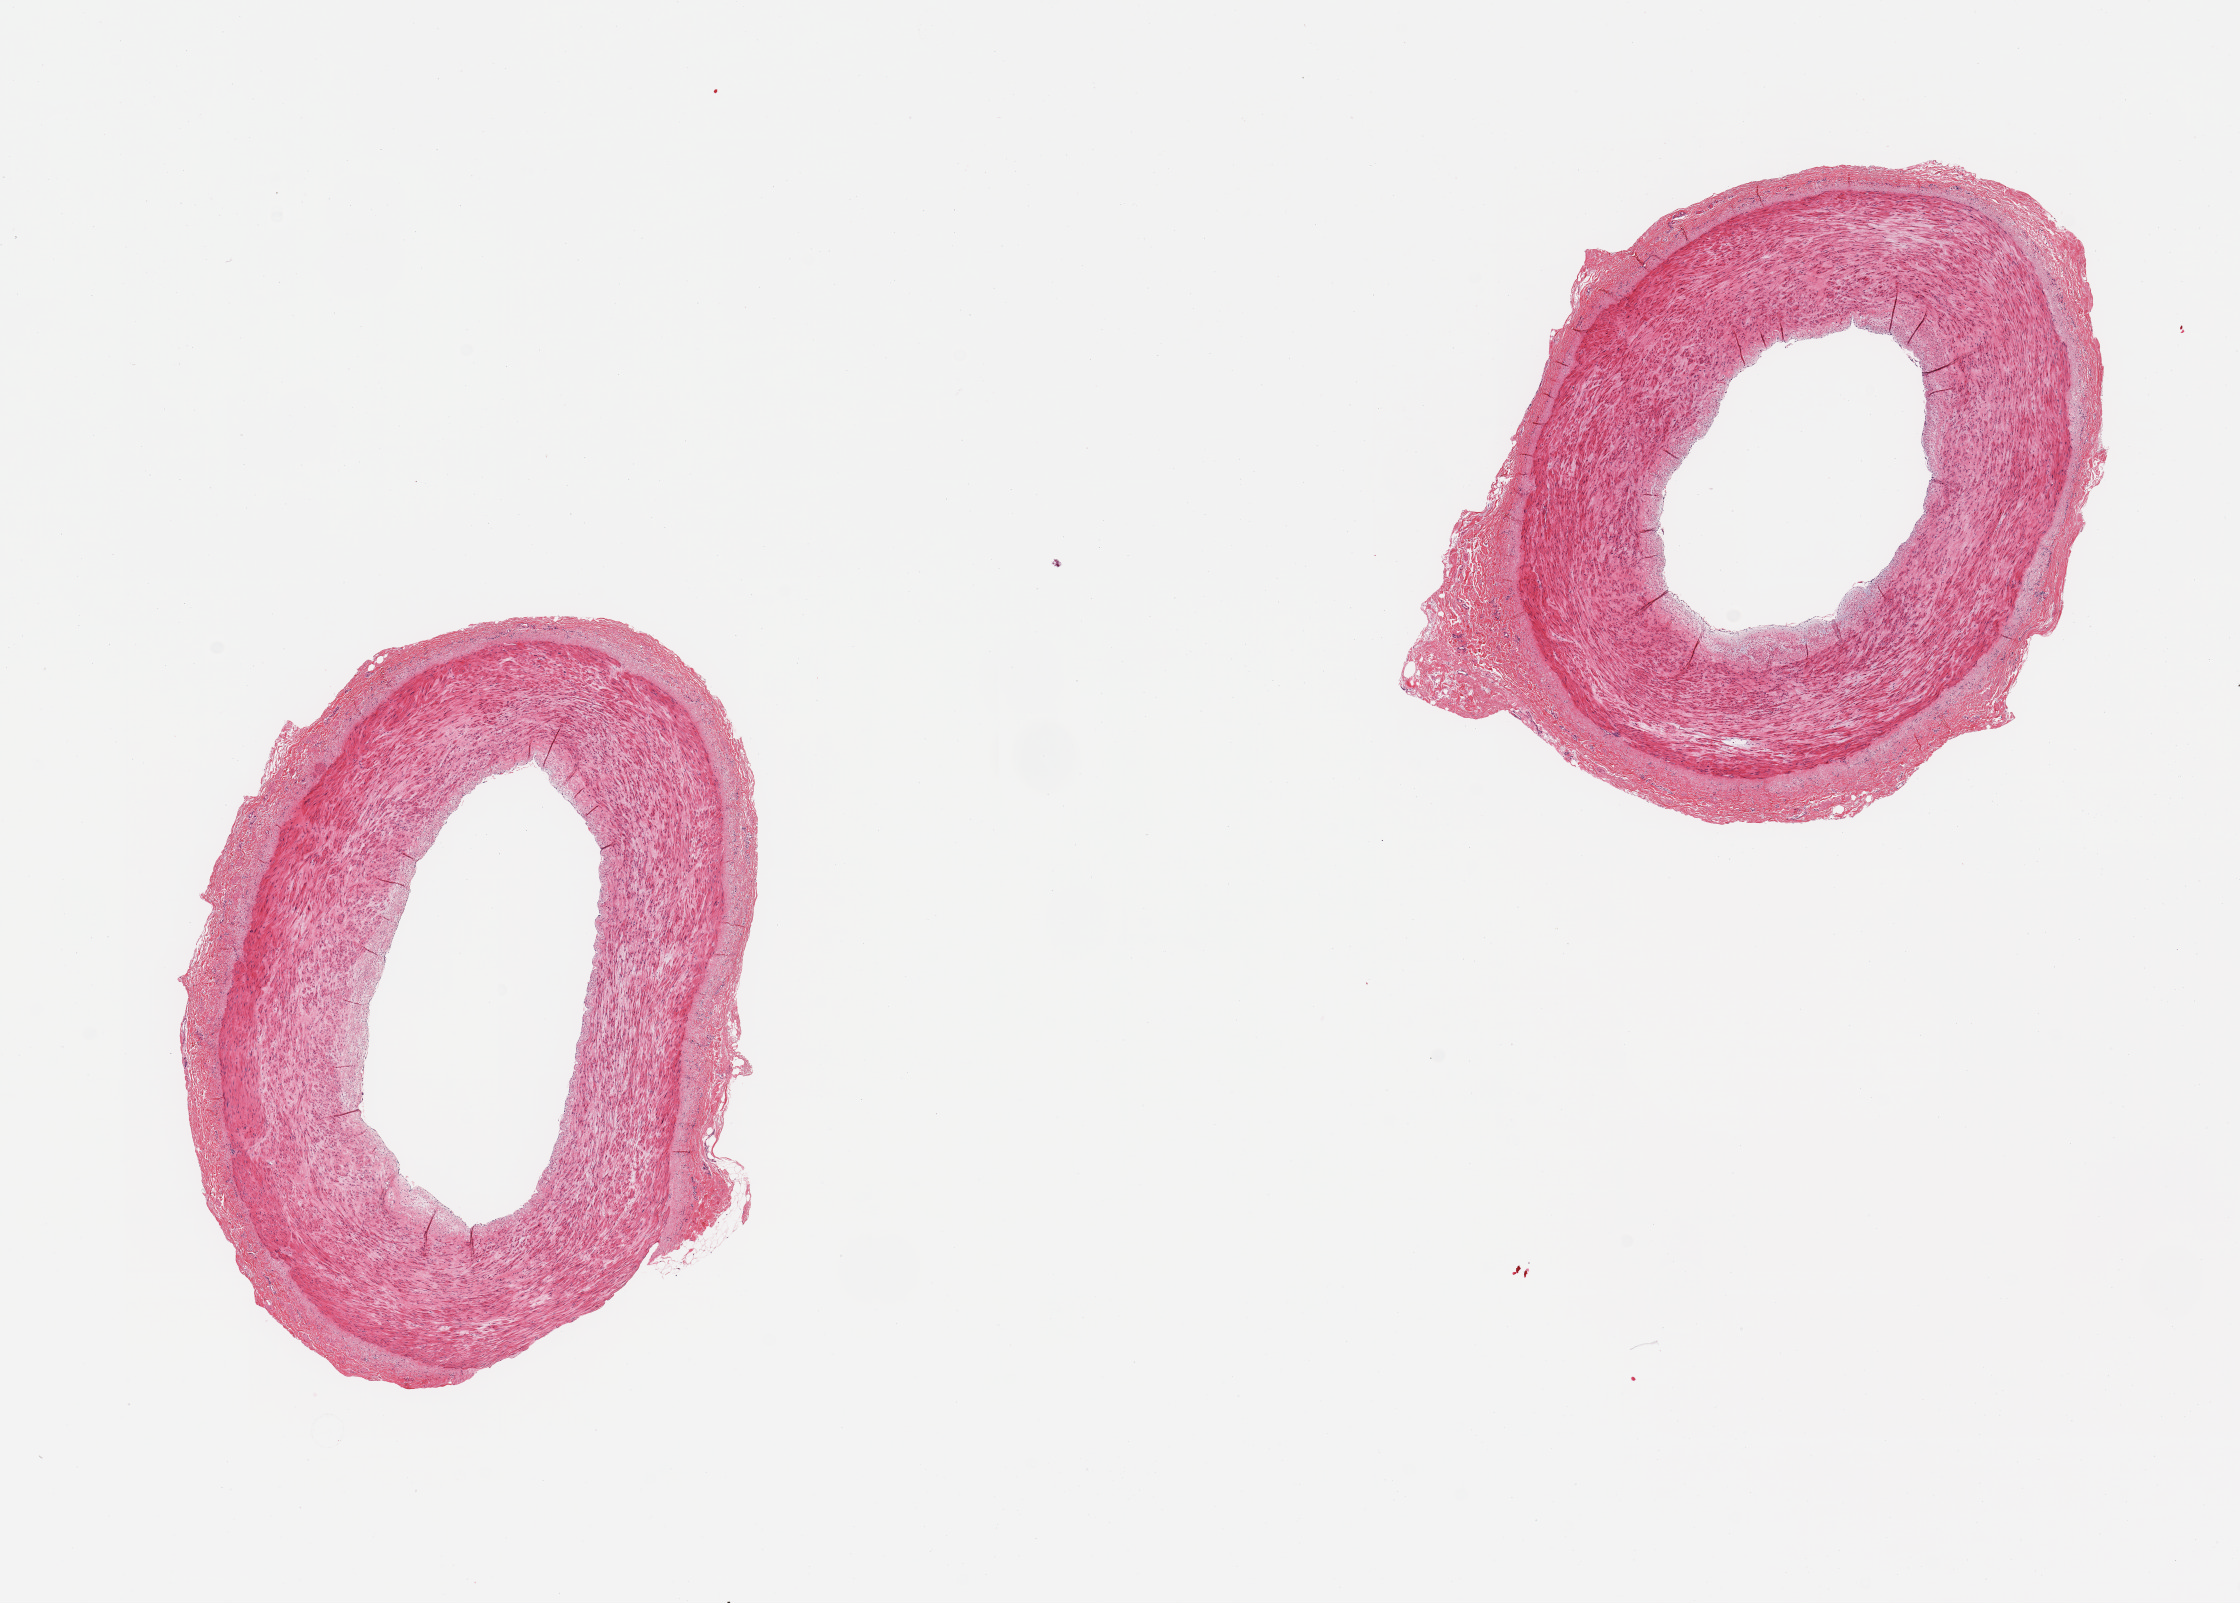
Digitized hematoxylin and eosin (H&E)-stained section, whole scanned area (about 17.7 x 12.7 mm, slide scanned at 20x) shown as a low-resolution overview; PAXgene-fixed, paraffin-embedded tissue; target tissue: tibial artery; donor tissue sample. Donor sex: male.
* pathologist's review note for this sample: 2 pieces; well trimmed, mild atherosclerosis